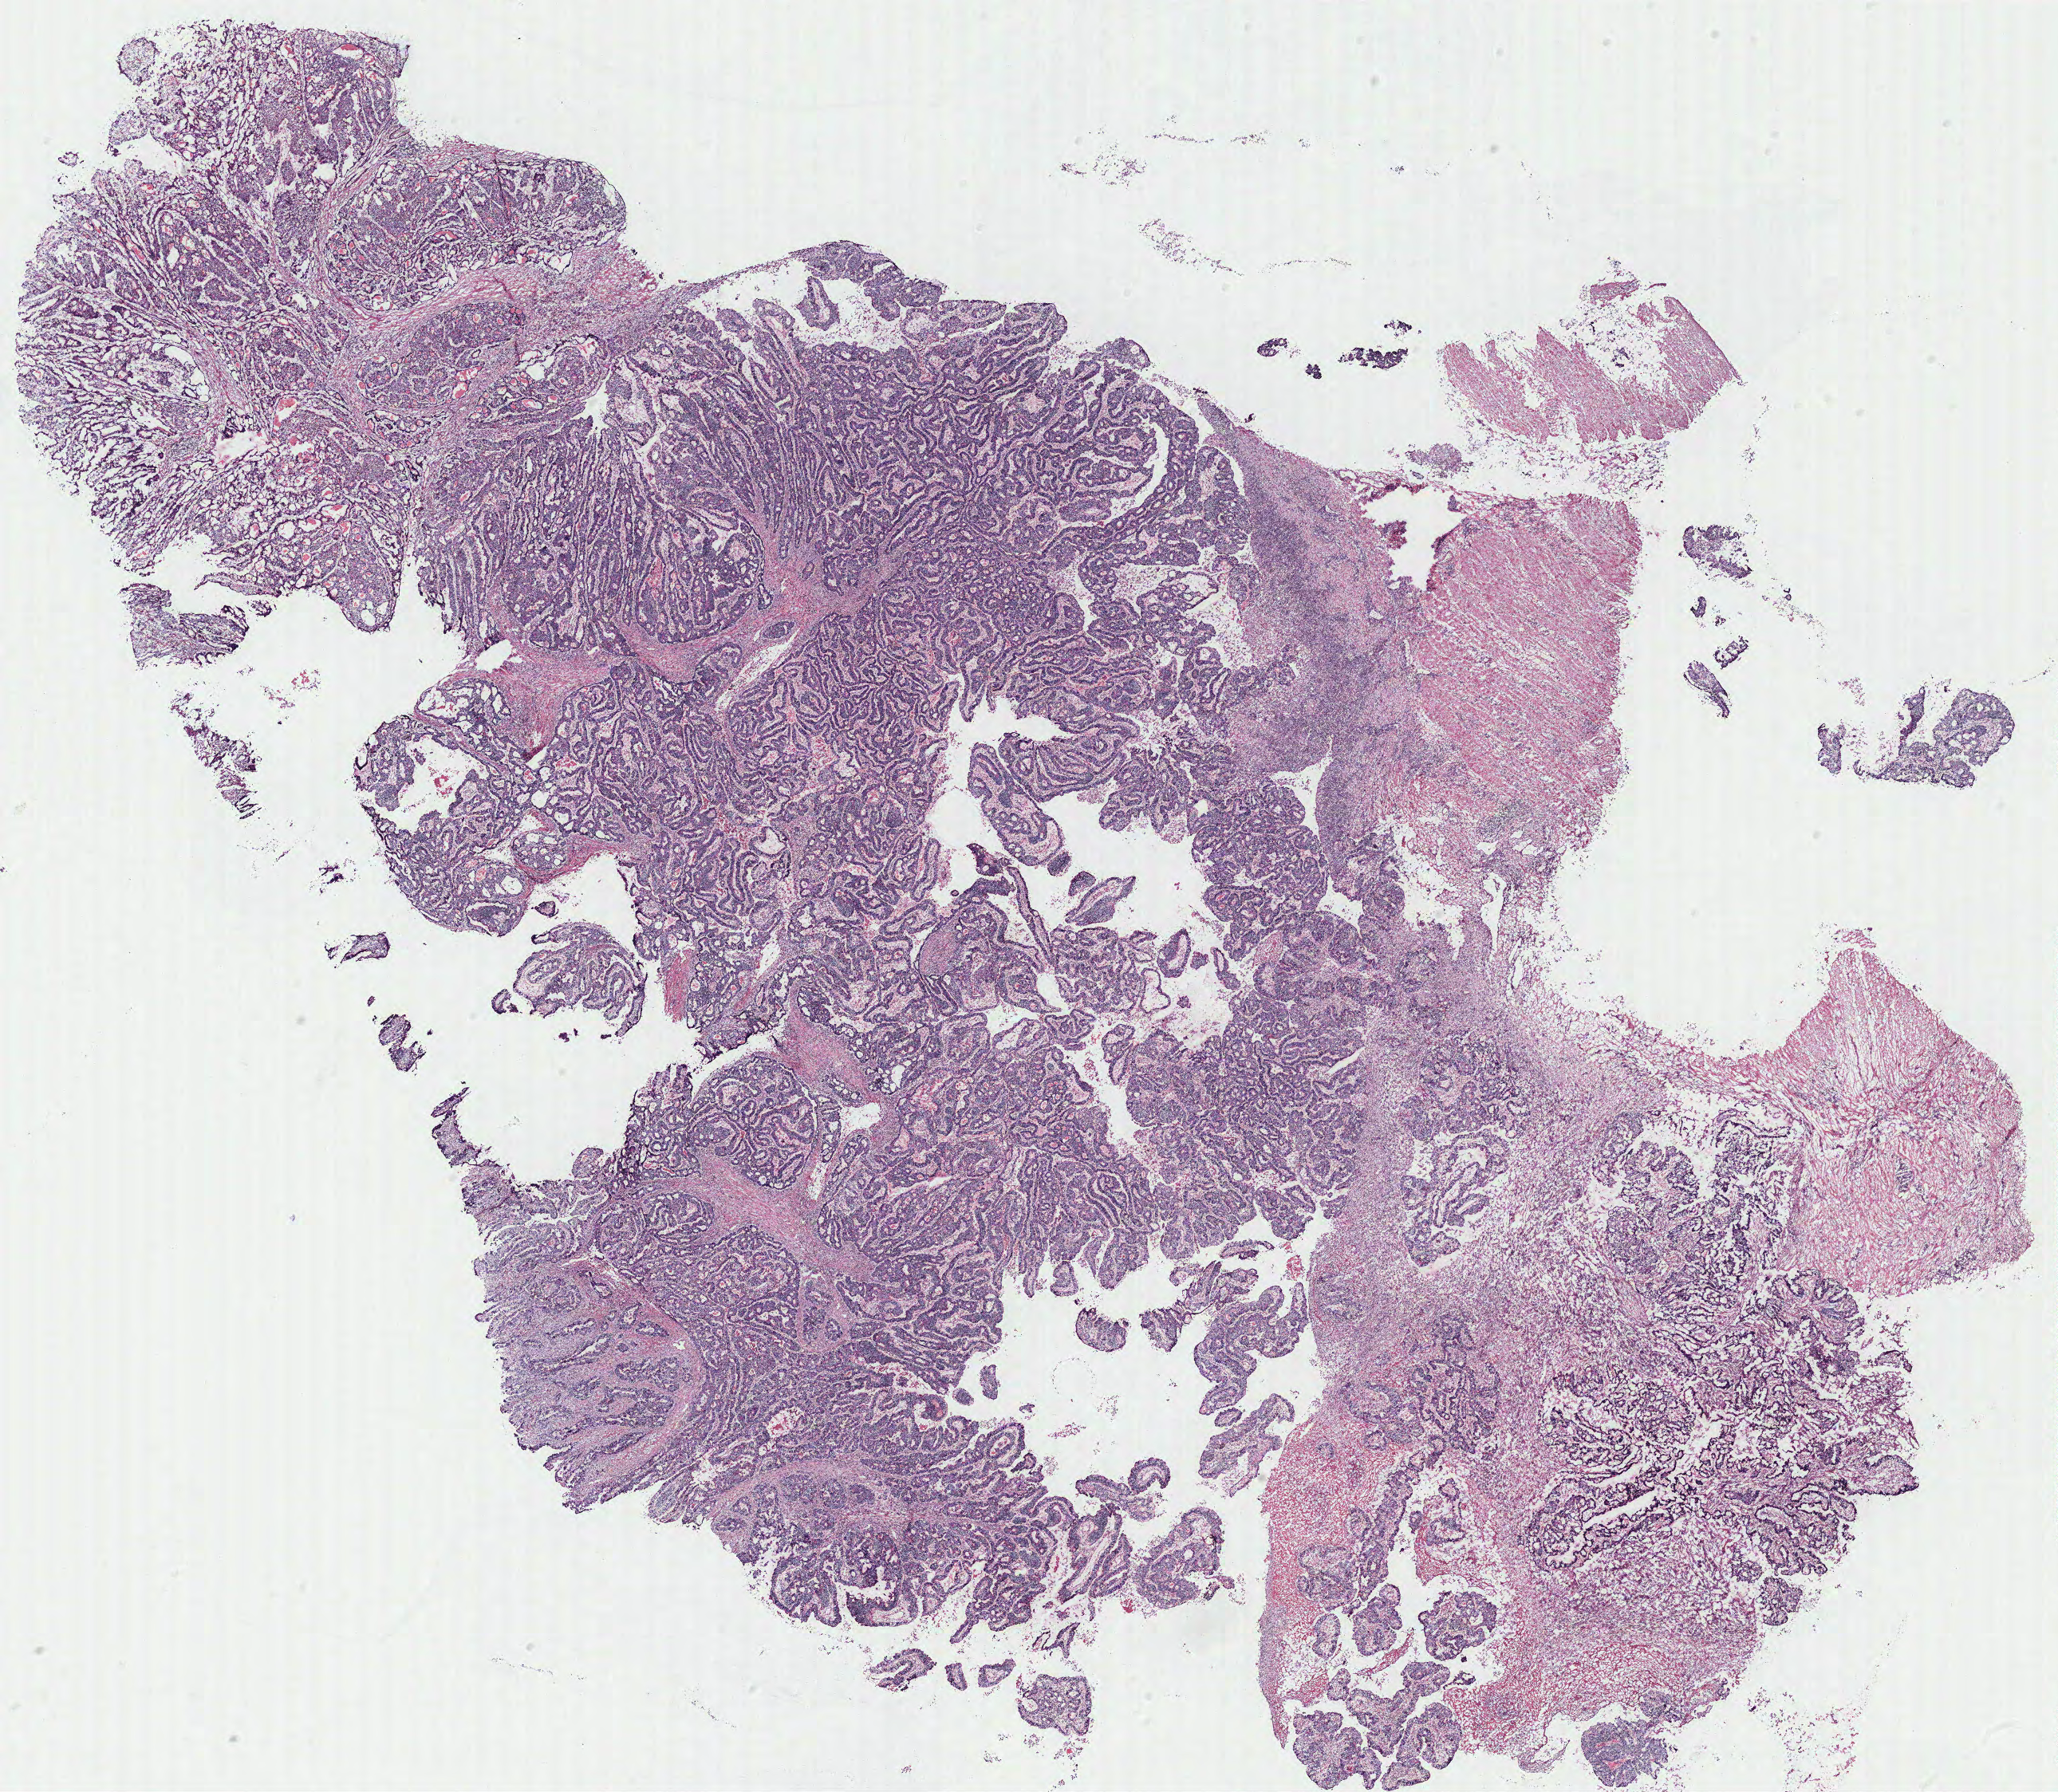
Whole-slide histology image, H&E-stained — low-resolution overview of the scanned area, about 20.6 x 18.0 mm (acquisition: 40x scan). Normal (non-tumour) tissue sample, colon. Female, 59 y/o.
This section: normal (non-tumour) tissue from the same patient. Patient diagnosis: Adenocarcinoma, NOS.